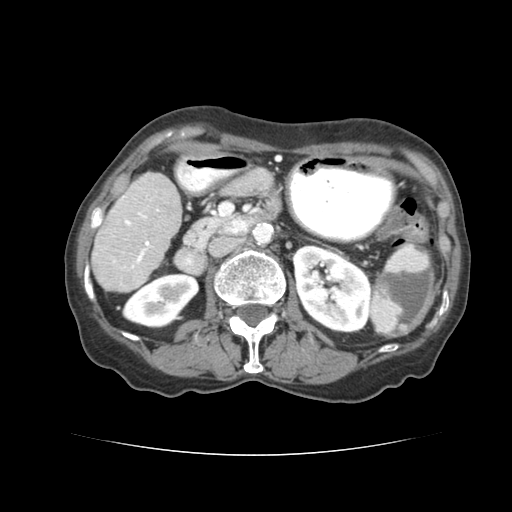
Contrast-enhanced abdominal CT (liver protocol), one axial slice; slice 22 of 77 in the series (ordered by position); reconstruction kernel STANDARD; 120 kVp; soft-tissue window (W 400 / L 40 HU); 2.5 mm slice thickness; 512 × 512 image matrix, field of view 340 × 340 mm. Case-level facts recorded for this patient, not image findings: diagnosis: hepatocellular carcinoma (patient treated with transarterial chemoembolisation; whether this scan precedes or follows treatment is not stated here); TNM stage (as recorded): Stage-I; Child-Pugh class: A; tumour differentiation: well differentiated; tumour nodularity: uninodular.
Outlined on this slice (semi-automatic segmentation, software-assisted and operator-edited):
- liver parenchyma outside the tumour (the mass and vessels are separate outlines, so this box may not span the whole liver): bounding box [x1, y1, x2, y2] px = [92, 170, 180, 290]
- liver vessels: [114, 192, 158, 275]